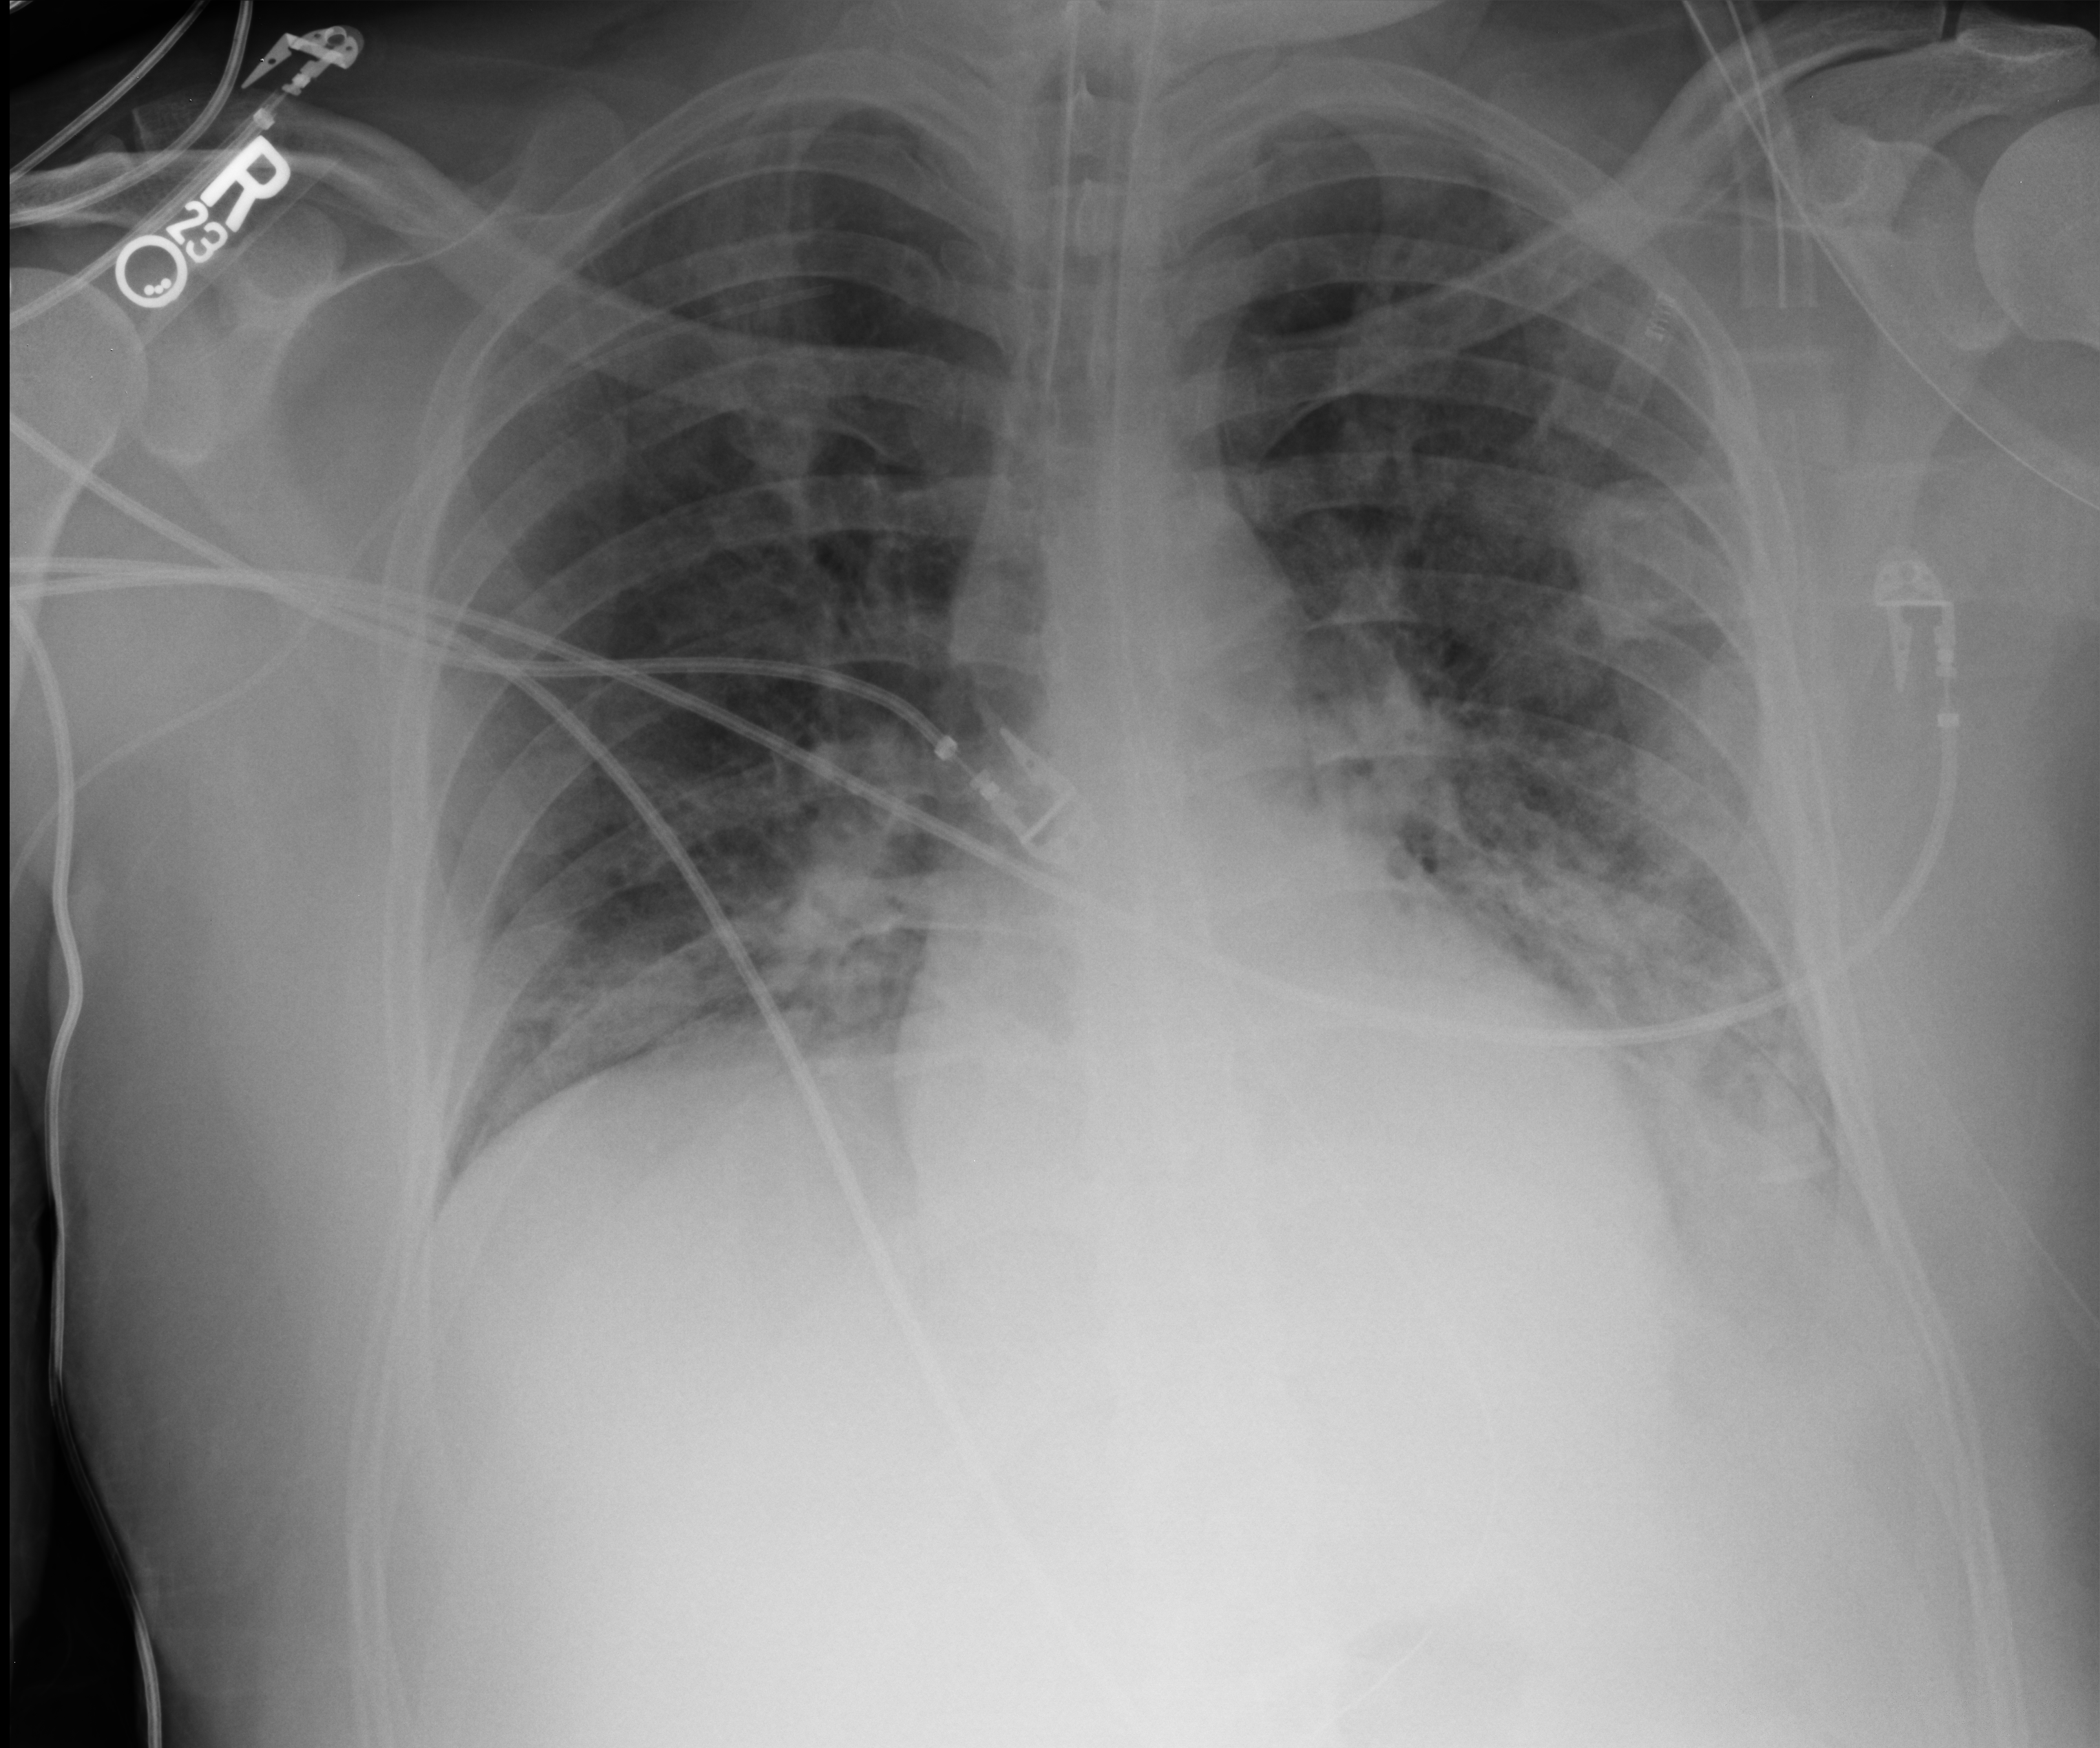
Portable chest radiograph; anteroposterior (AP) projection. Patient hospitalised with COVID-19; male, aged 18–59 years.
From the hospital-stay record, not from the radiograph (when in the stay this image was taken is not recorded): admitted to intensive care during this hospital stay: yes; diabetes (admission record): no; mechanically ventilated during this hospital stay: yes.